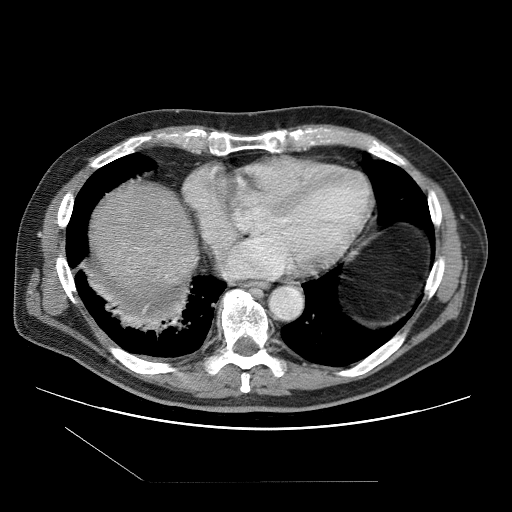
Contrast-enhanced abdominal CT (liver protocol), one axial slice. Position 98 of 109 along the scan axis. Reconstruction kernel STANDARD. 120 kVp. One of 2 acquisitions stored at this slice position. Soft-tissue window (W 400 / L 40 HU). 2.5 mm slice thickness. 512 × 512 image matrix, field of view 400 × 400 mm. From the clinical record (not read from this slice): diagnosis: hepatocellular carcinoma (patient treated with transarterial chemoembolisation; whether this scan precedes or follows treatment is not stated here); TNM stage (as recorded): Stage-IIIB; Child-Pugh class: A; tumour differentiation: well differentiated; tumour nodularity: multinodular.
Outlined on this slice (semi-automatic segmentation, software-assisted and operator-edited):
- liver parenchyma outside the tumour (the mass and vessels are separate outlines, so this box may not span the whole liver): box from (x=90, y=182) to (x=198, y=304) px